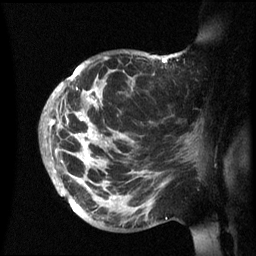
Breast MRI (dynamic contrast-enhanced), one sagittal slice. Dynamic contrast-enhanced series, image 2 of 3 at this slice position (ordered by acquisition). 1.5 T. TE 4.2 ms, TR 8.4 ms. 2.4 mm slice thickness. 256 × 256 image matrix. Female patient, age 48 years.
Outlined on this slice (semi-automatically segmented with operator editing):
- analysis volume of interest (the breast-tissue region the enhancement analysis was run in; not a lesion): box from (x=42, y=52) to (x=202, y=236) px
- tumour enhancement mask (voxels above the 70 % enhancement threshold inside the analysis volume of interest): (x=45, y=56)–(x=173, y=203)